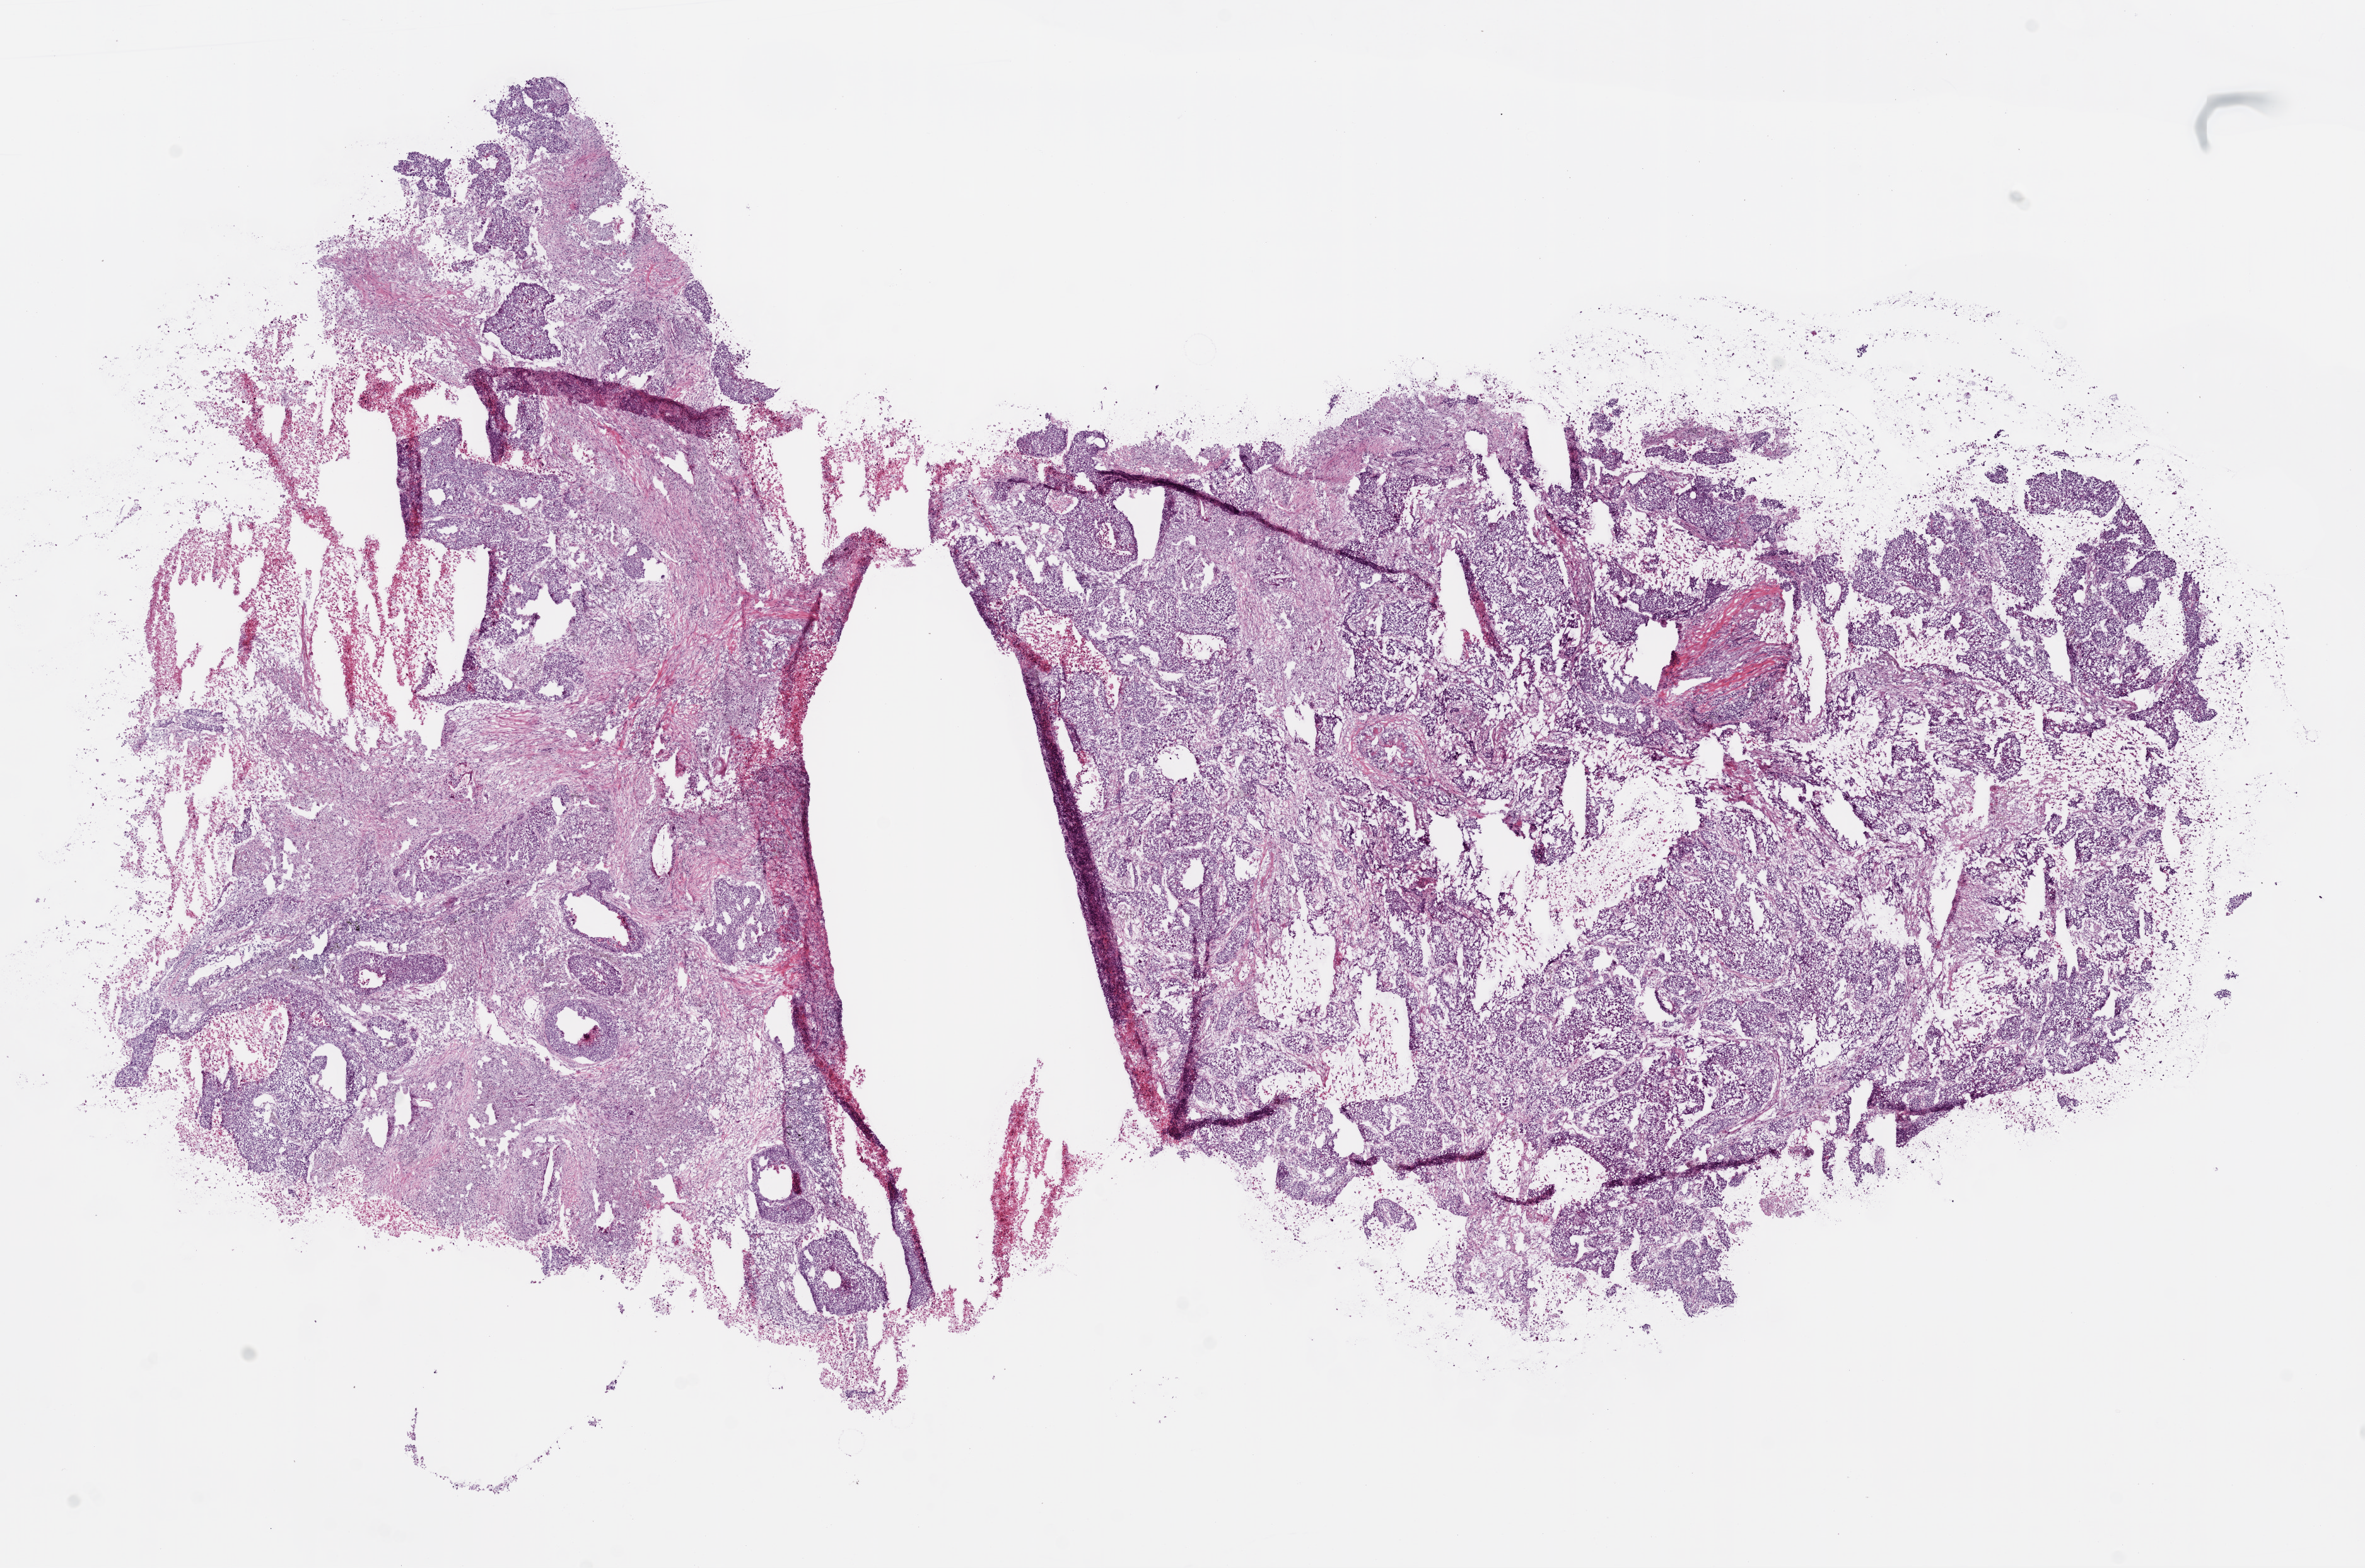
Digitized H&E-stained tissue section (whole slide), shown as a low-resolution overview of the whole scanned area (about 15.0 x 10.0 mm, acquisition: 20x scan), frozen section, primary tumour sample from the lung. Female patient; age at initial diagnosis 73 years. Pathologist review of this section (percent, as recorded): tumour cells 70%, tumour nuclei 80%, normal cells 0%, stromal cells 15%, necrosis 15%.
- AJCC pathologic stage: IIB (6th edition)
- laterality: left
- diagnosis: Basaloid squamous cell carcinoma (upper lobe, lung)